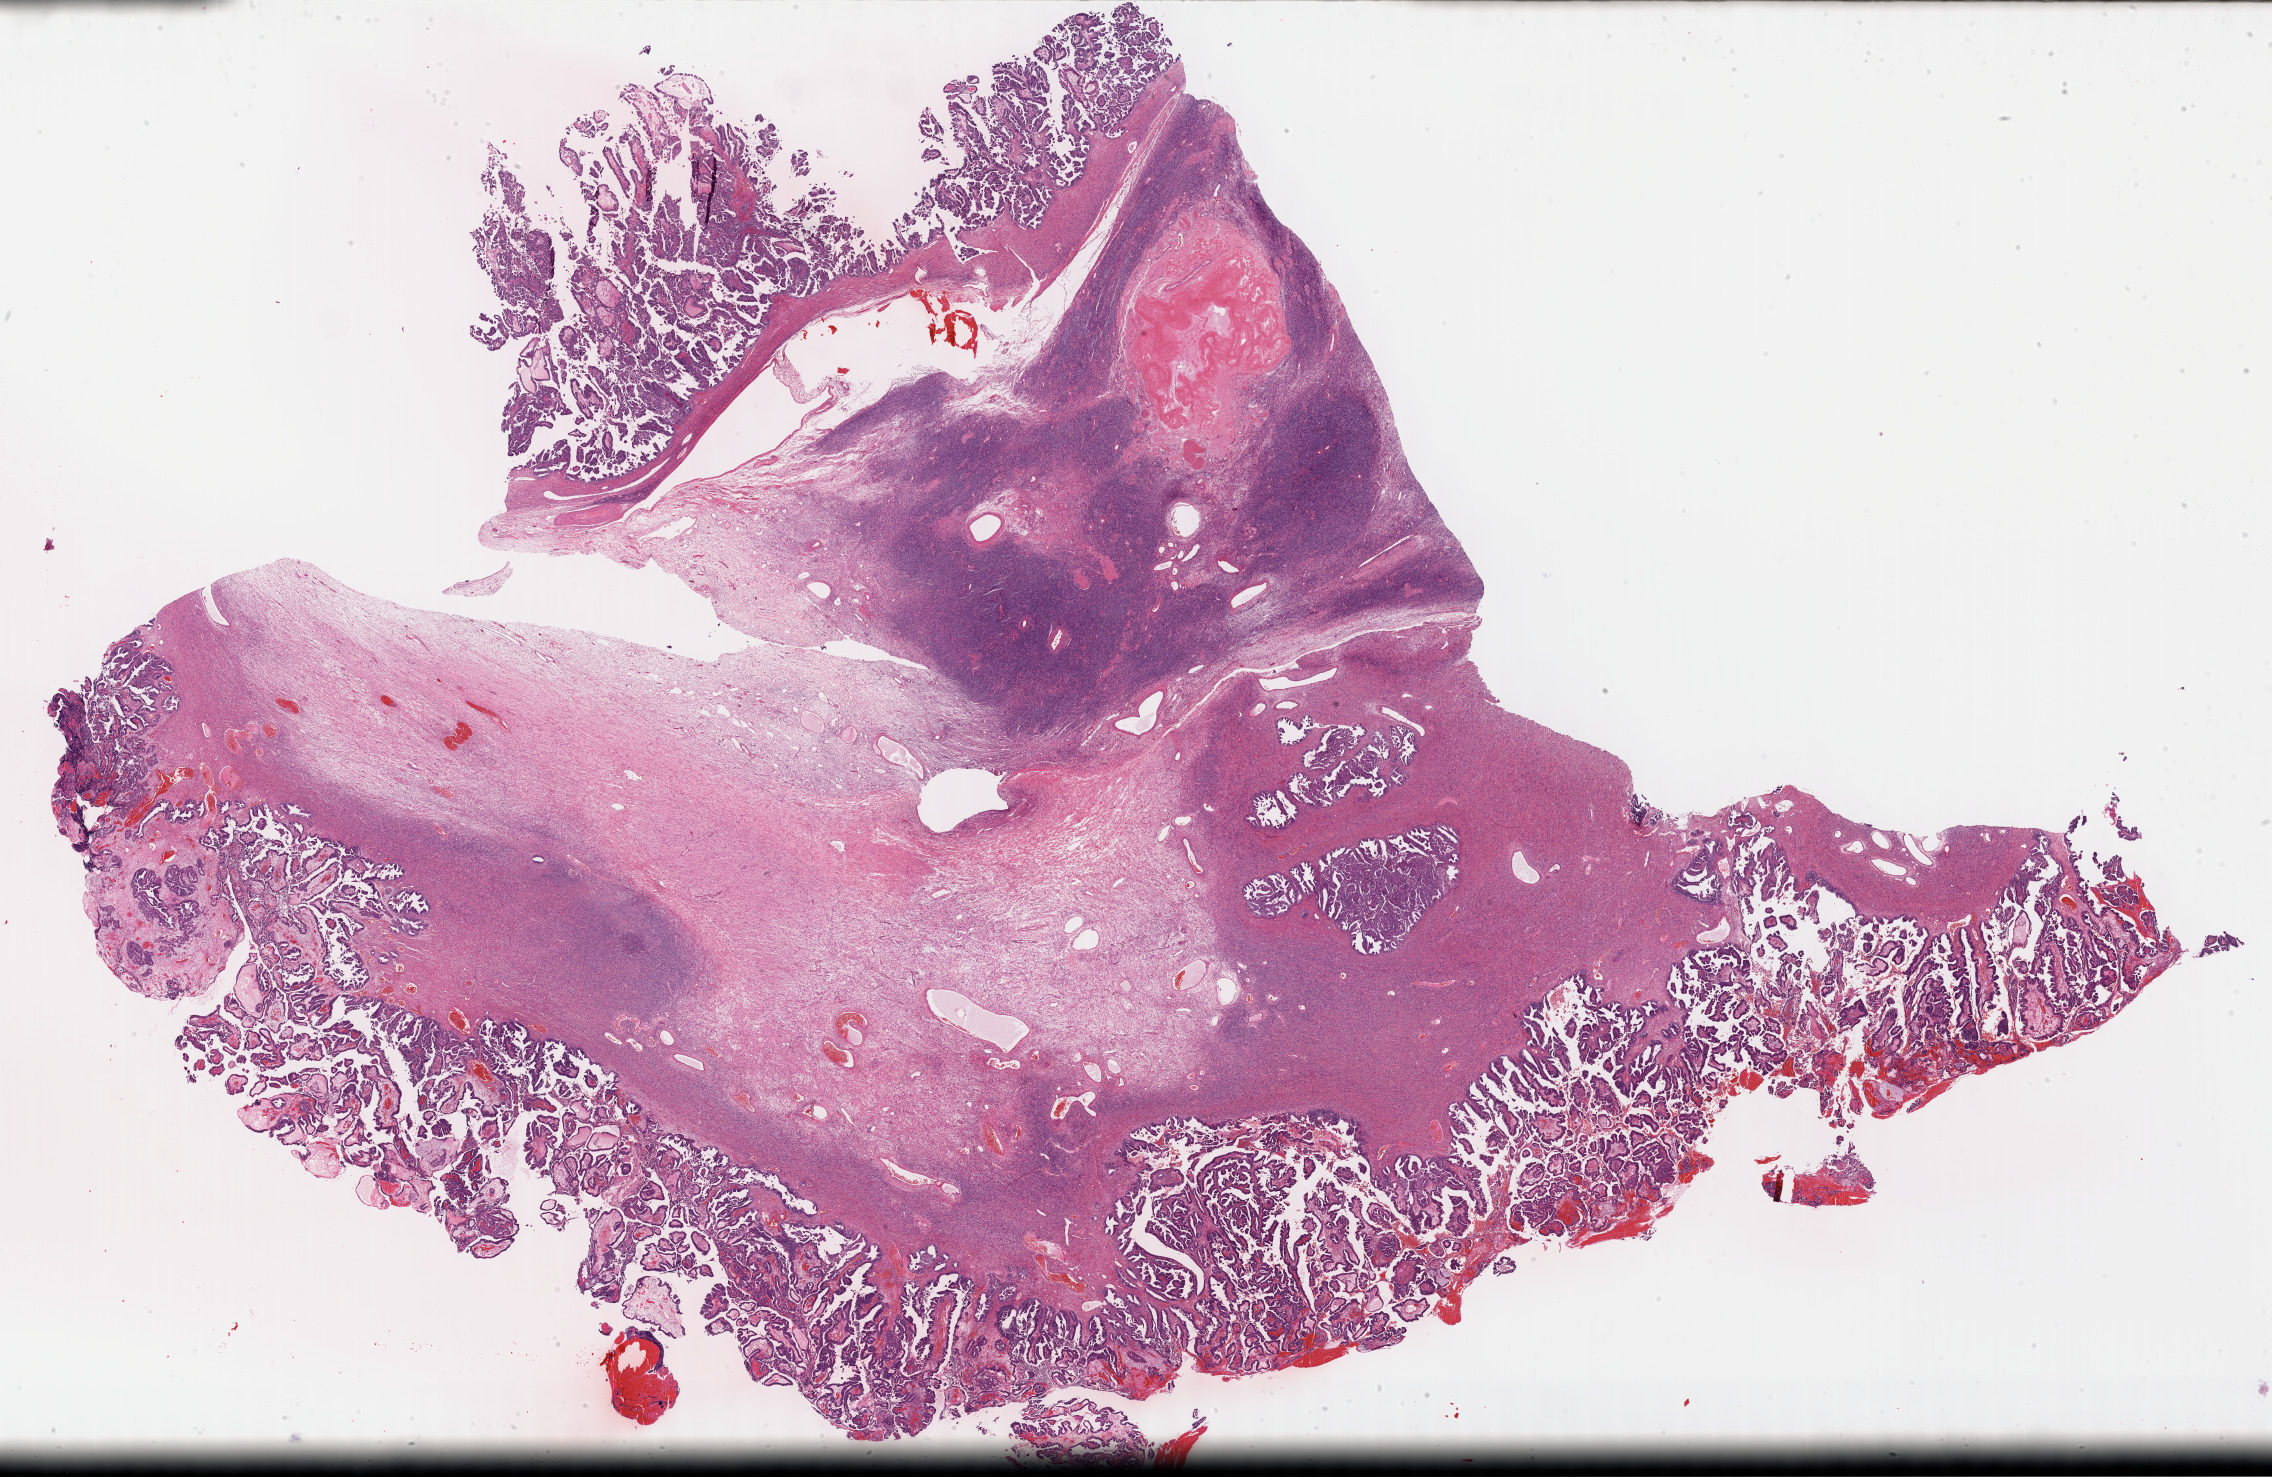
Digitized H&E-stained tissue section (whole slide) — a low-resolution overview of the entire scanned area, about 36.7 x 23.9 mm (acquisition: 40x scan); formalin-fixed paraffin-embedded (FFPE) diagnostic section; primary tumour sample from the ovary. Female patient; age at initial diagnosis 55 years. Histologic grade: G3 (poorly differentiated).
Histologic diagnosis: Serous cystadenocarcinoma, NOS. FIGO stage: IIIC. Laterality: left.